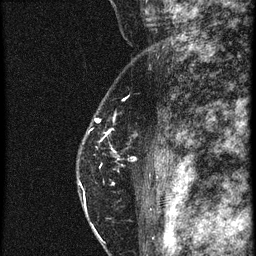
Breast MRI (dynamic contrast-enhanced), one sagittal slice; slice 43 of 60 in the series (ordered by position); 4 images stored at this slice position (order not interpretable as contrast timing); 1.5 T; TE 4.2 ms, TR 20.4 ms; 1.5 mm slice thickness; 256 × 256 image matrix. Female patient, age 46 years. Case-level facts recorded for this patient, not image findings: setting: breast cancer imaged before/during neoadjuvant chemotherapy; receptor status: triple-negative.
Outlined on this slice (semi-automatic segmentation, software-assisted and operator-edited):
- analysis volume of interest (the breast-tissue region the enhancement analysis was run in; not a lesion): bounding box (x1, y1, x2, y2) in pixels: (76, 82, 159, 201)
- tumour enhancement mask (voxels above the 90 % enhancement threshold inside the analysis volume of interest): (80, 132, 159, 187)